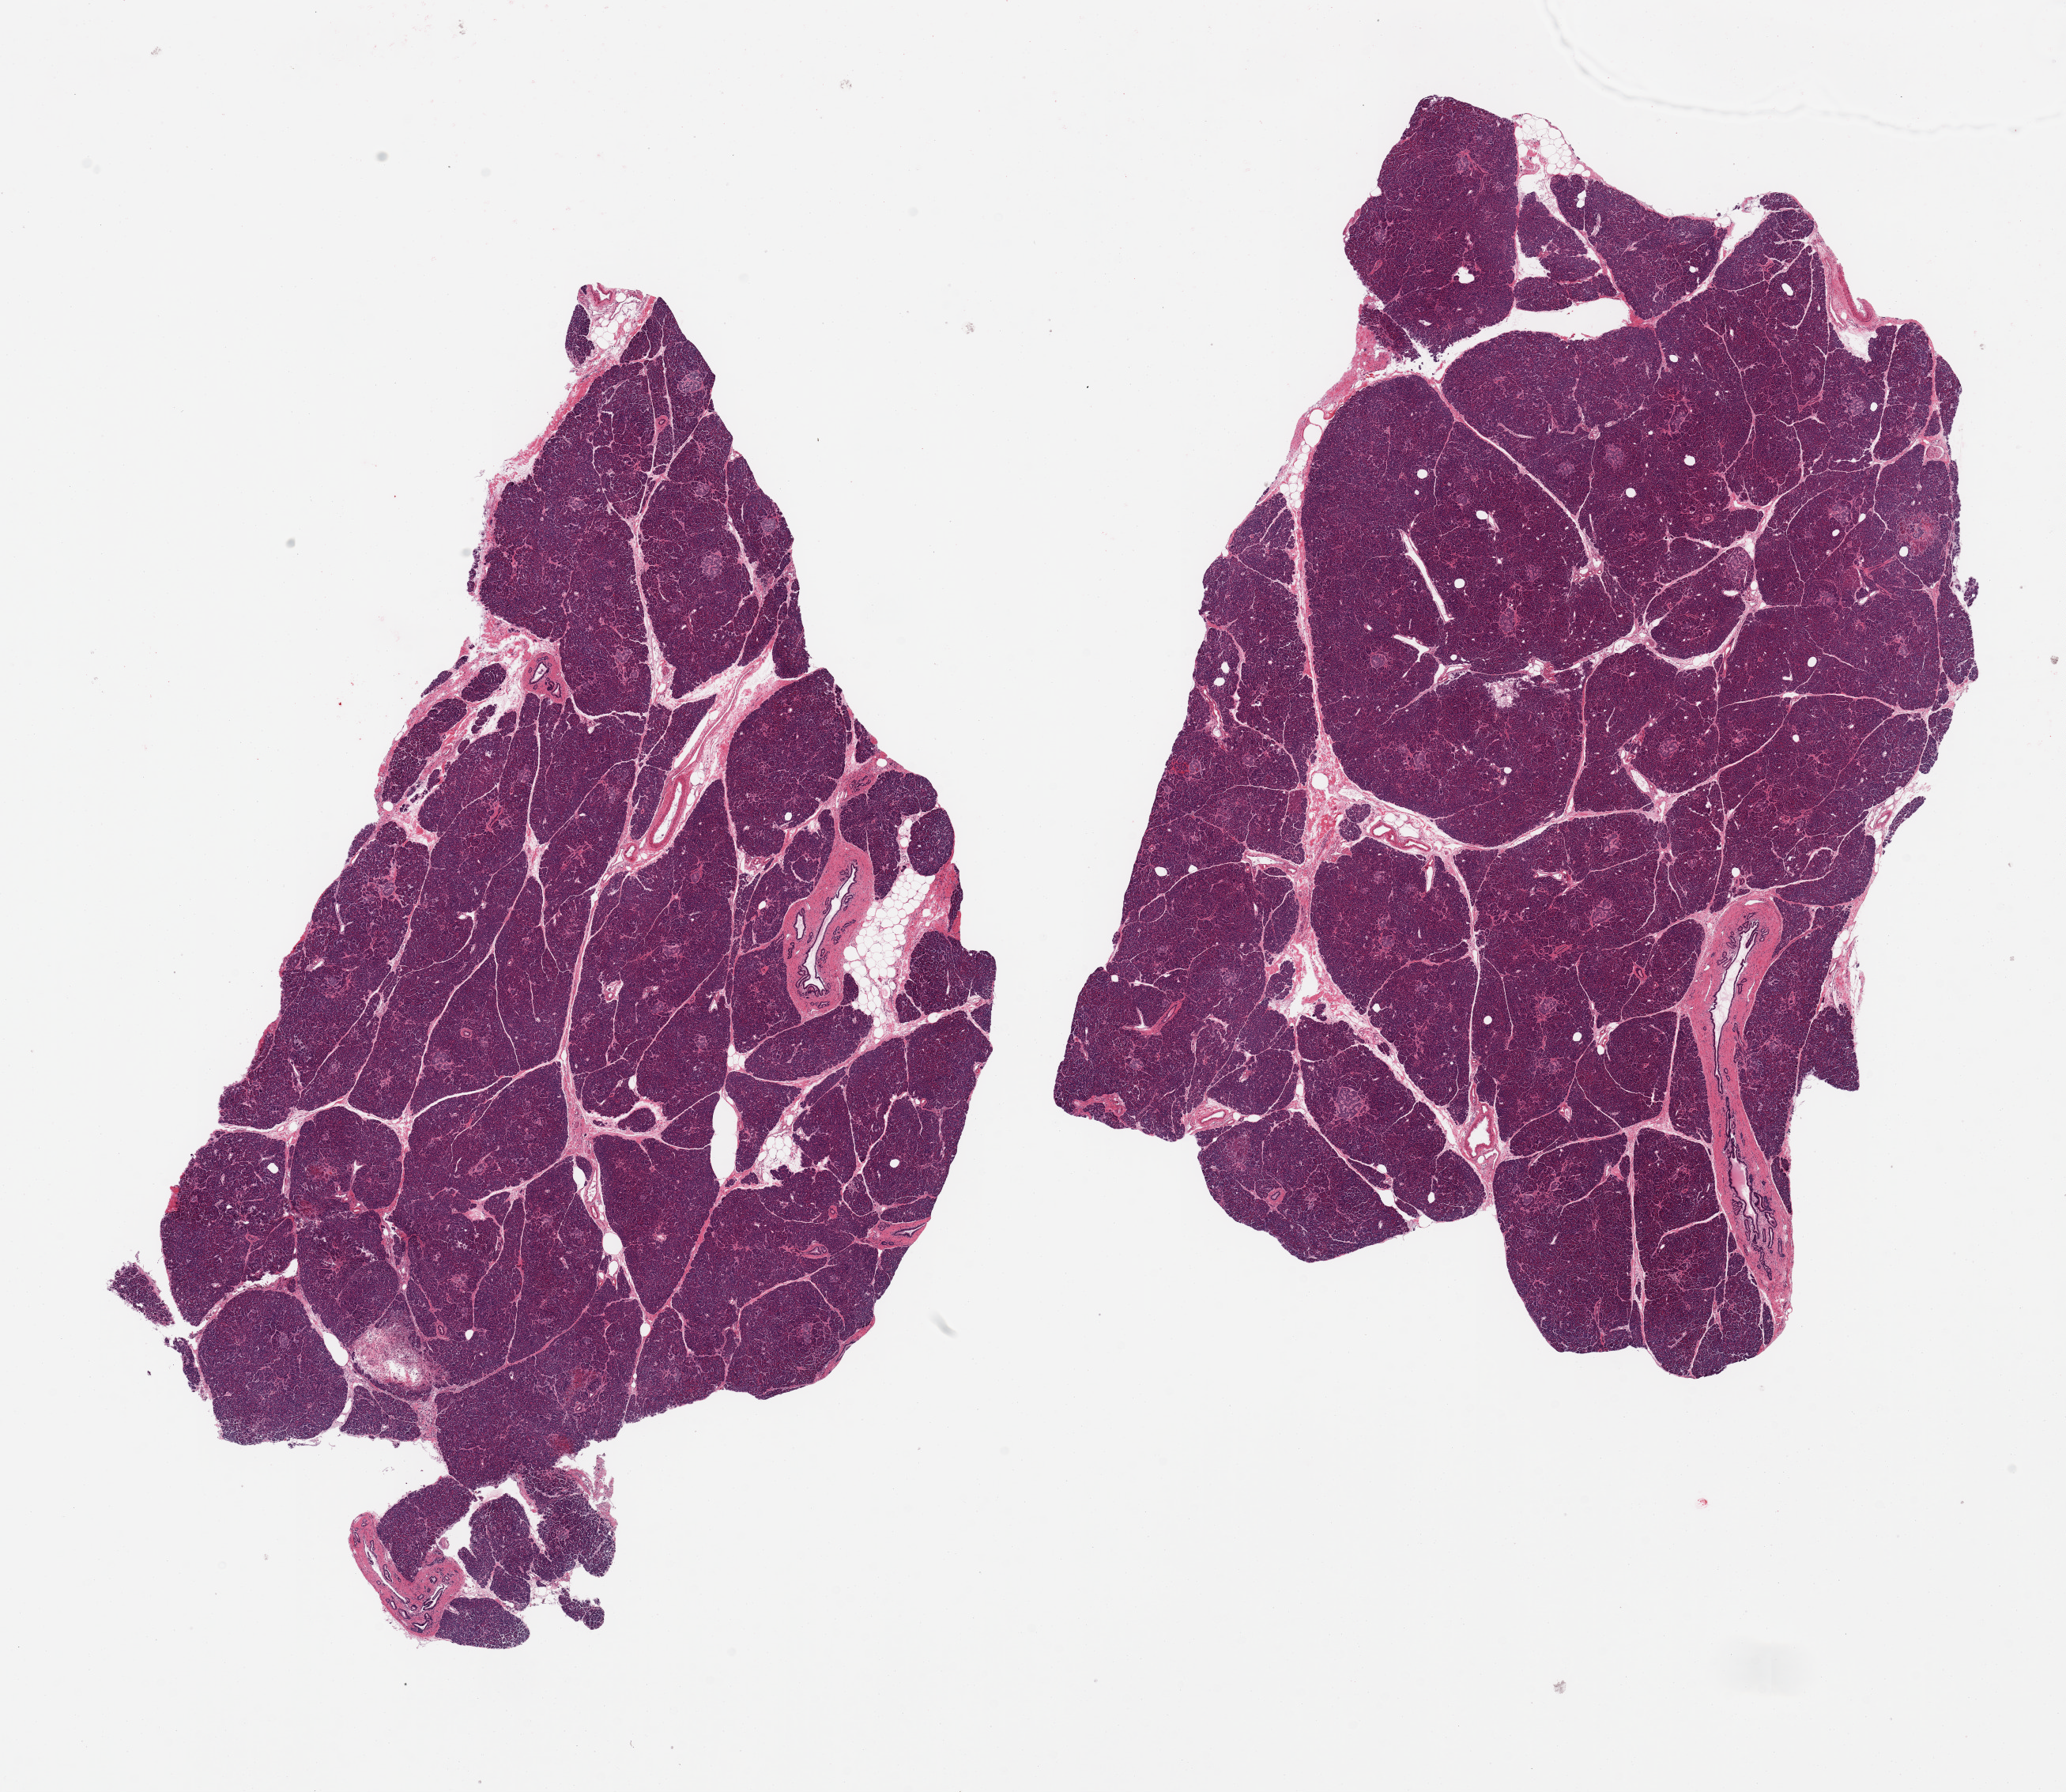
Whole-slide image, haematoxylin and eosin stain, low-resolution overview of the scanned area, about 20.7 x 17.9 mm, PAXgene-fixed paraffin-embedded (PFPE) section, sampled site (target tissue): pancreas, donor tissue sample. Female donor.
Reviewer comment on this tissue sample: 2 pieces; well preserved, islets well visualized, focal acute pancreatitis.